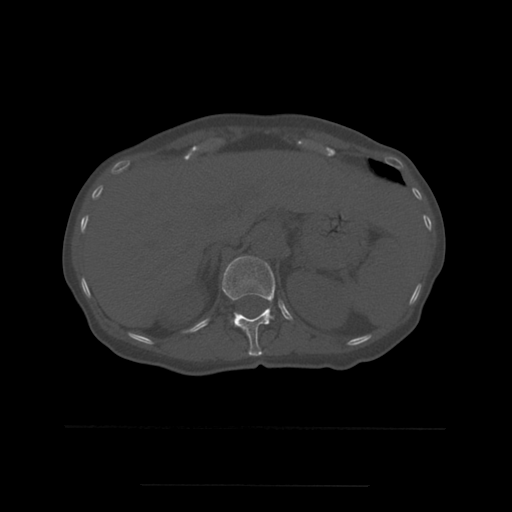
CT including the spine, one axial slice. Position 255 of 544 along the scan axis. Bone window (W 1800 / L 400 HU). 1.25 mm slice thickness. 512 × 512 image matrix, field of view 350 × 350 mm. Patient age 58 years. Case-level facts recorded for this patient, not image findings: primary cancer: lung.
Annotated regions visible in this slice (semi-automatic segmentation, software-assisted and operator-edited):
- L1 vertebra: bounding box [x1, y1, x2, y2] px = [232, 320, 236, 326]
- T12 vertebra: [222, 256, 276, 356]